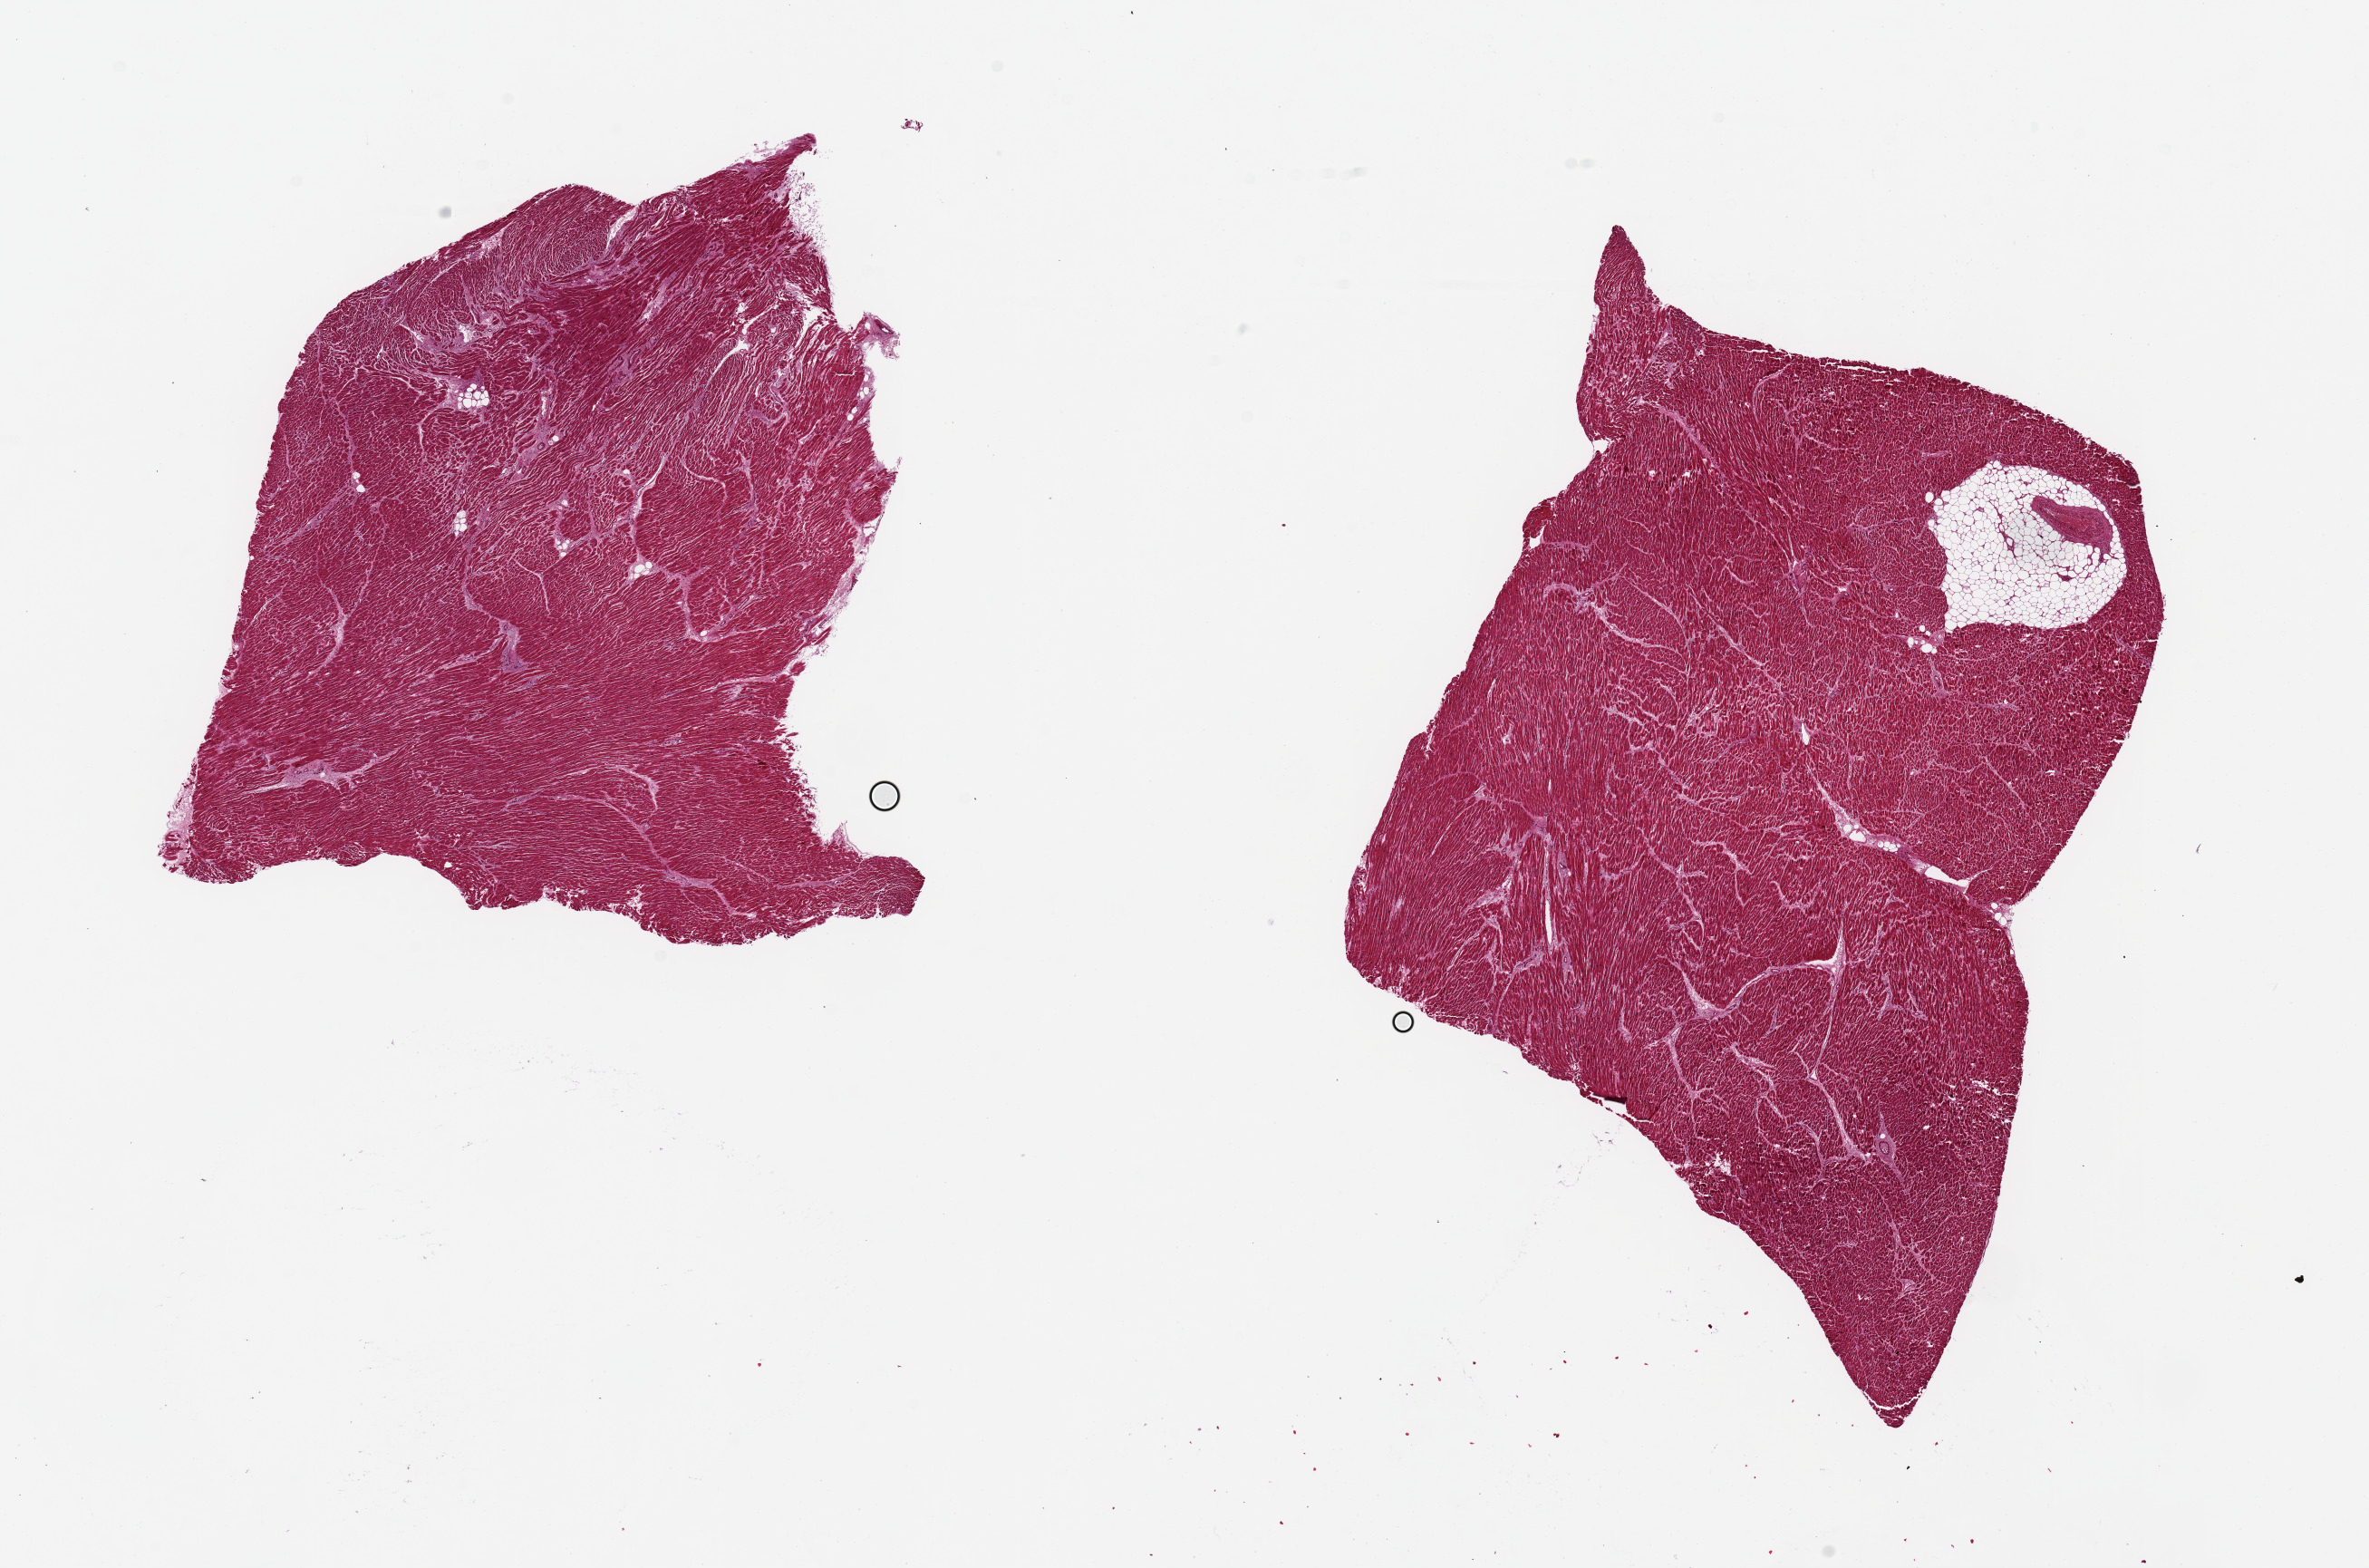
Whole-slide image, H&E stain, brightfield, shown as a low-resolution overview of the whole scanned area (about 20.7 x 13.7 mm); PAXgene-fixed, paraffin-embedded tissue; target tissue: heart; donor tissue sample.
Pathologist's review note for this sample: 2 pieces, 7x7 & 9x7mm; minimal ischemic change.